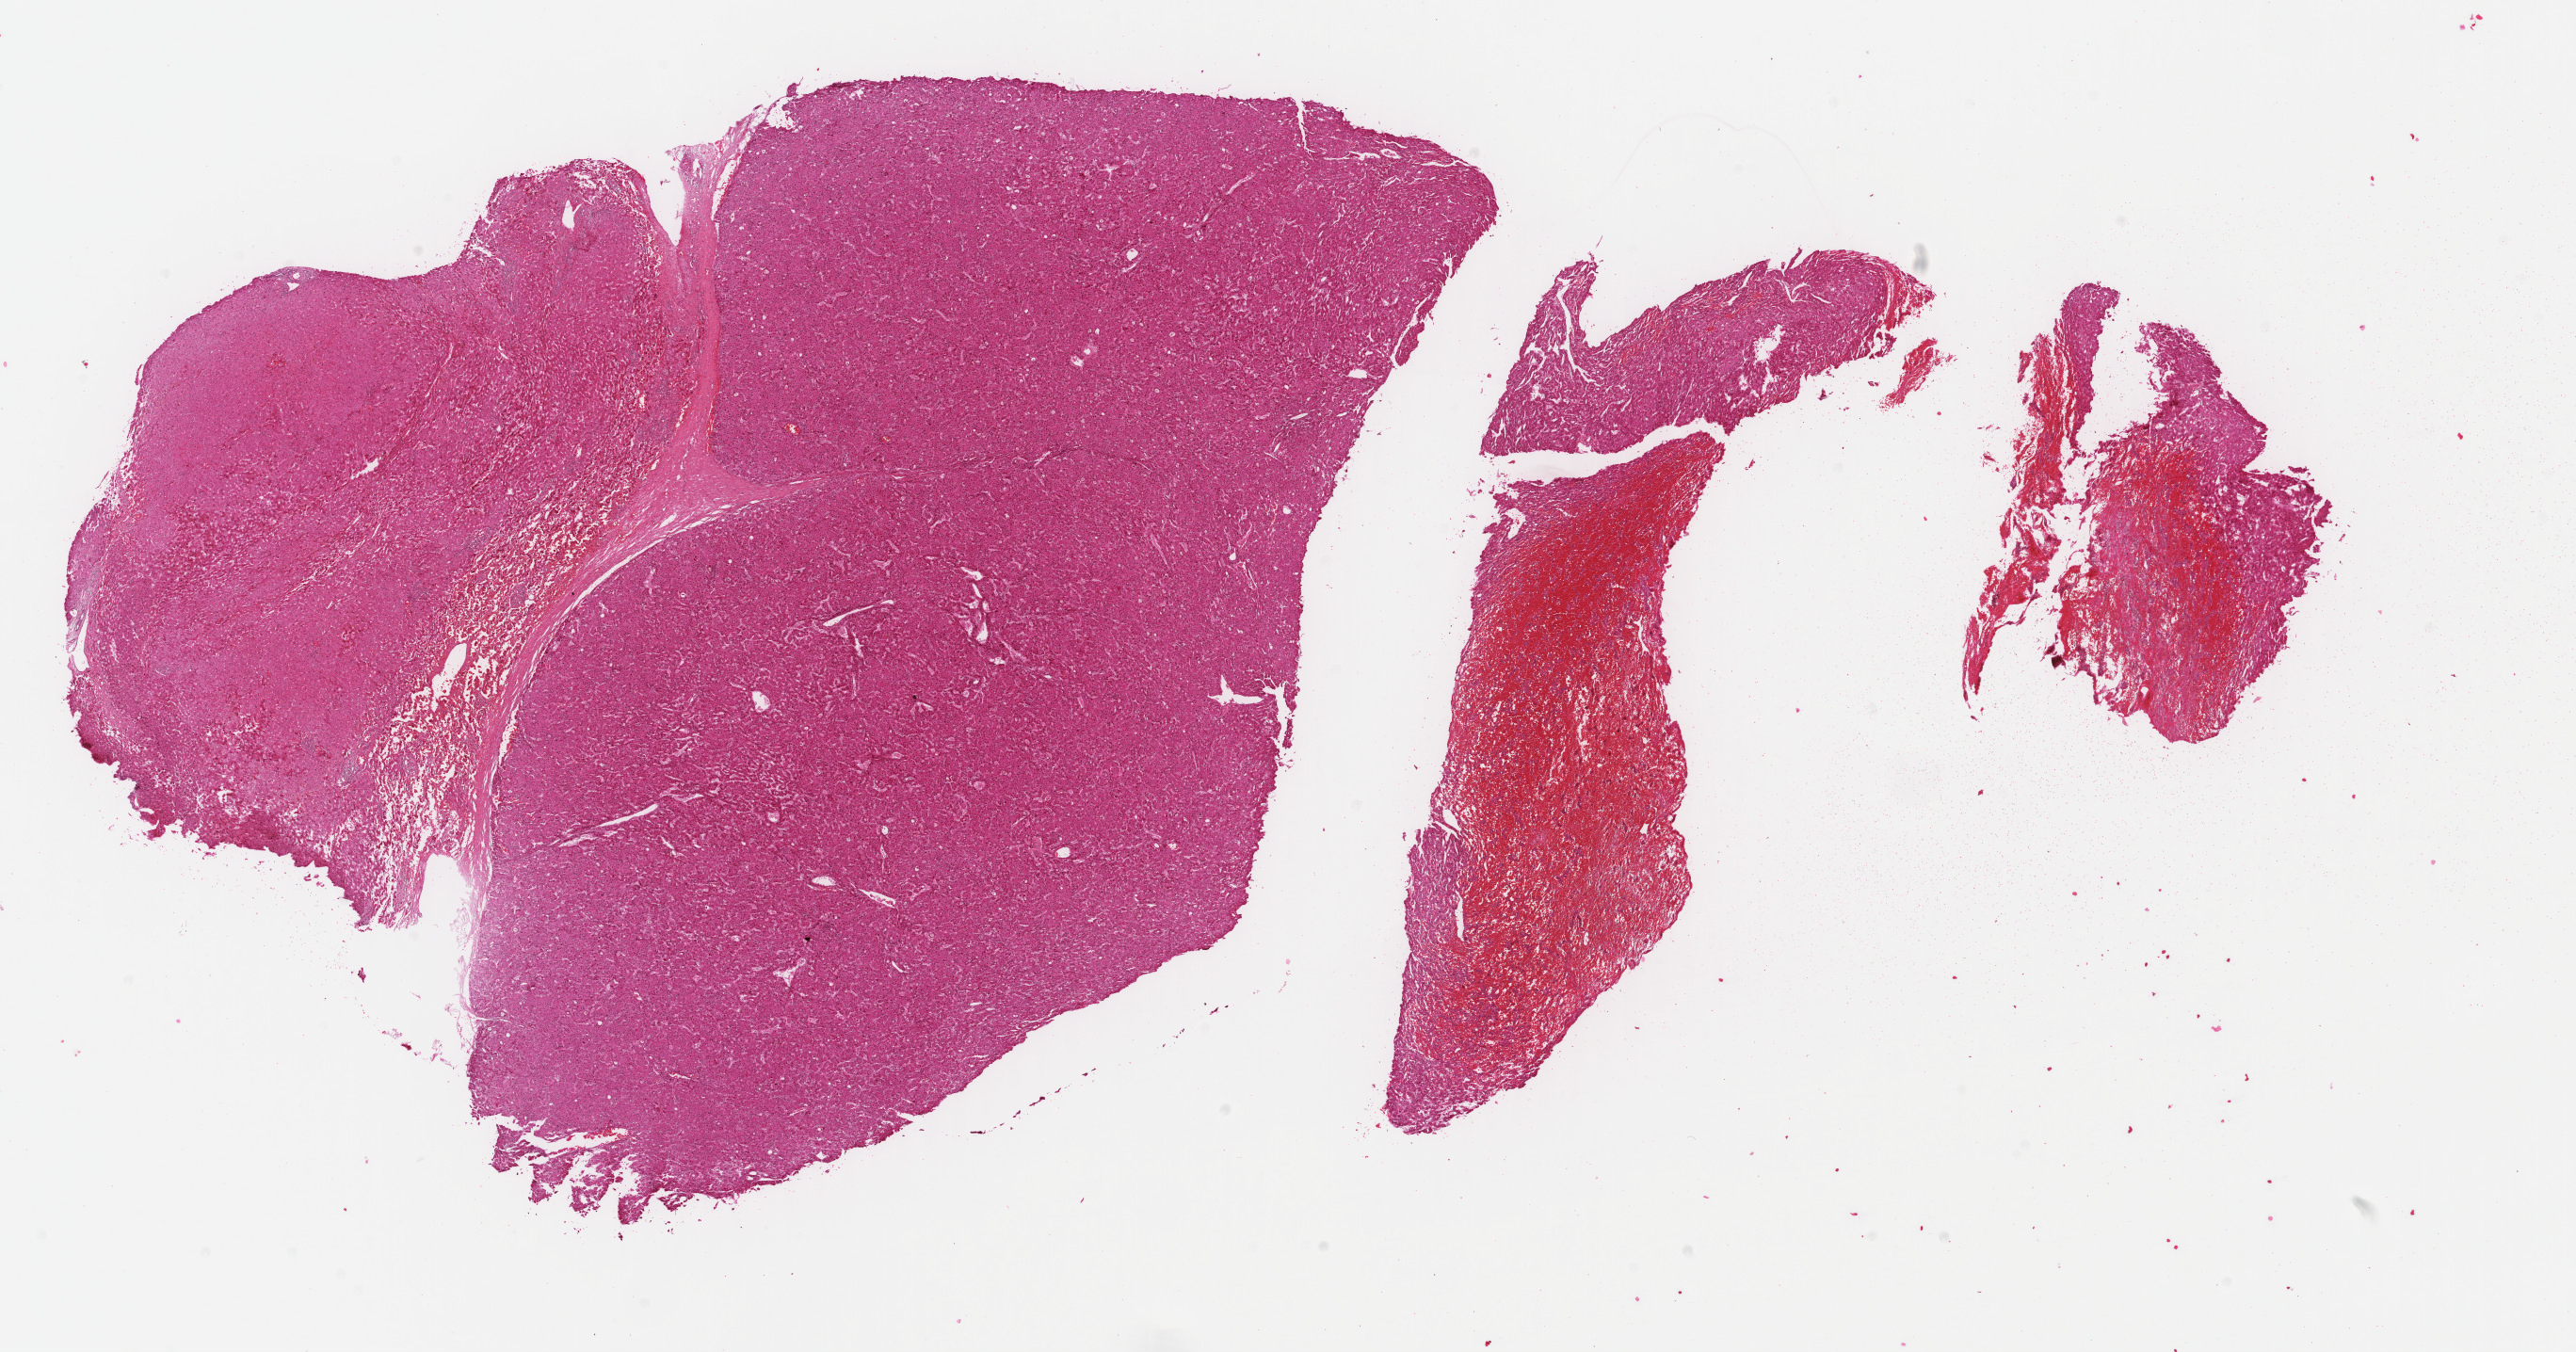
Whole-slide histology image, H&E, low-resolution overview of the scanned area, about 21.7 x 11.4 mm, FFPE section, sample: primary tumour, liver. Patient: male, age at initial diagnosis 81 years. Histologic grade: G1 (well differentiated).
- diagnosis: Hepatocellular carcinoma, NOS